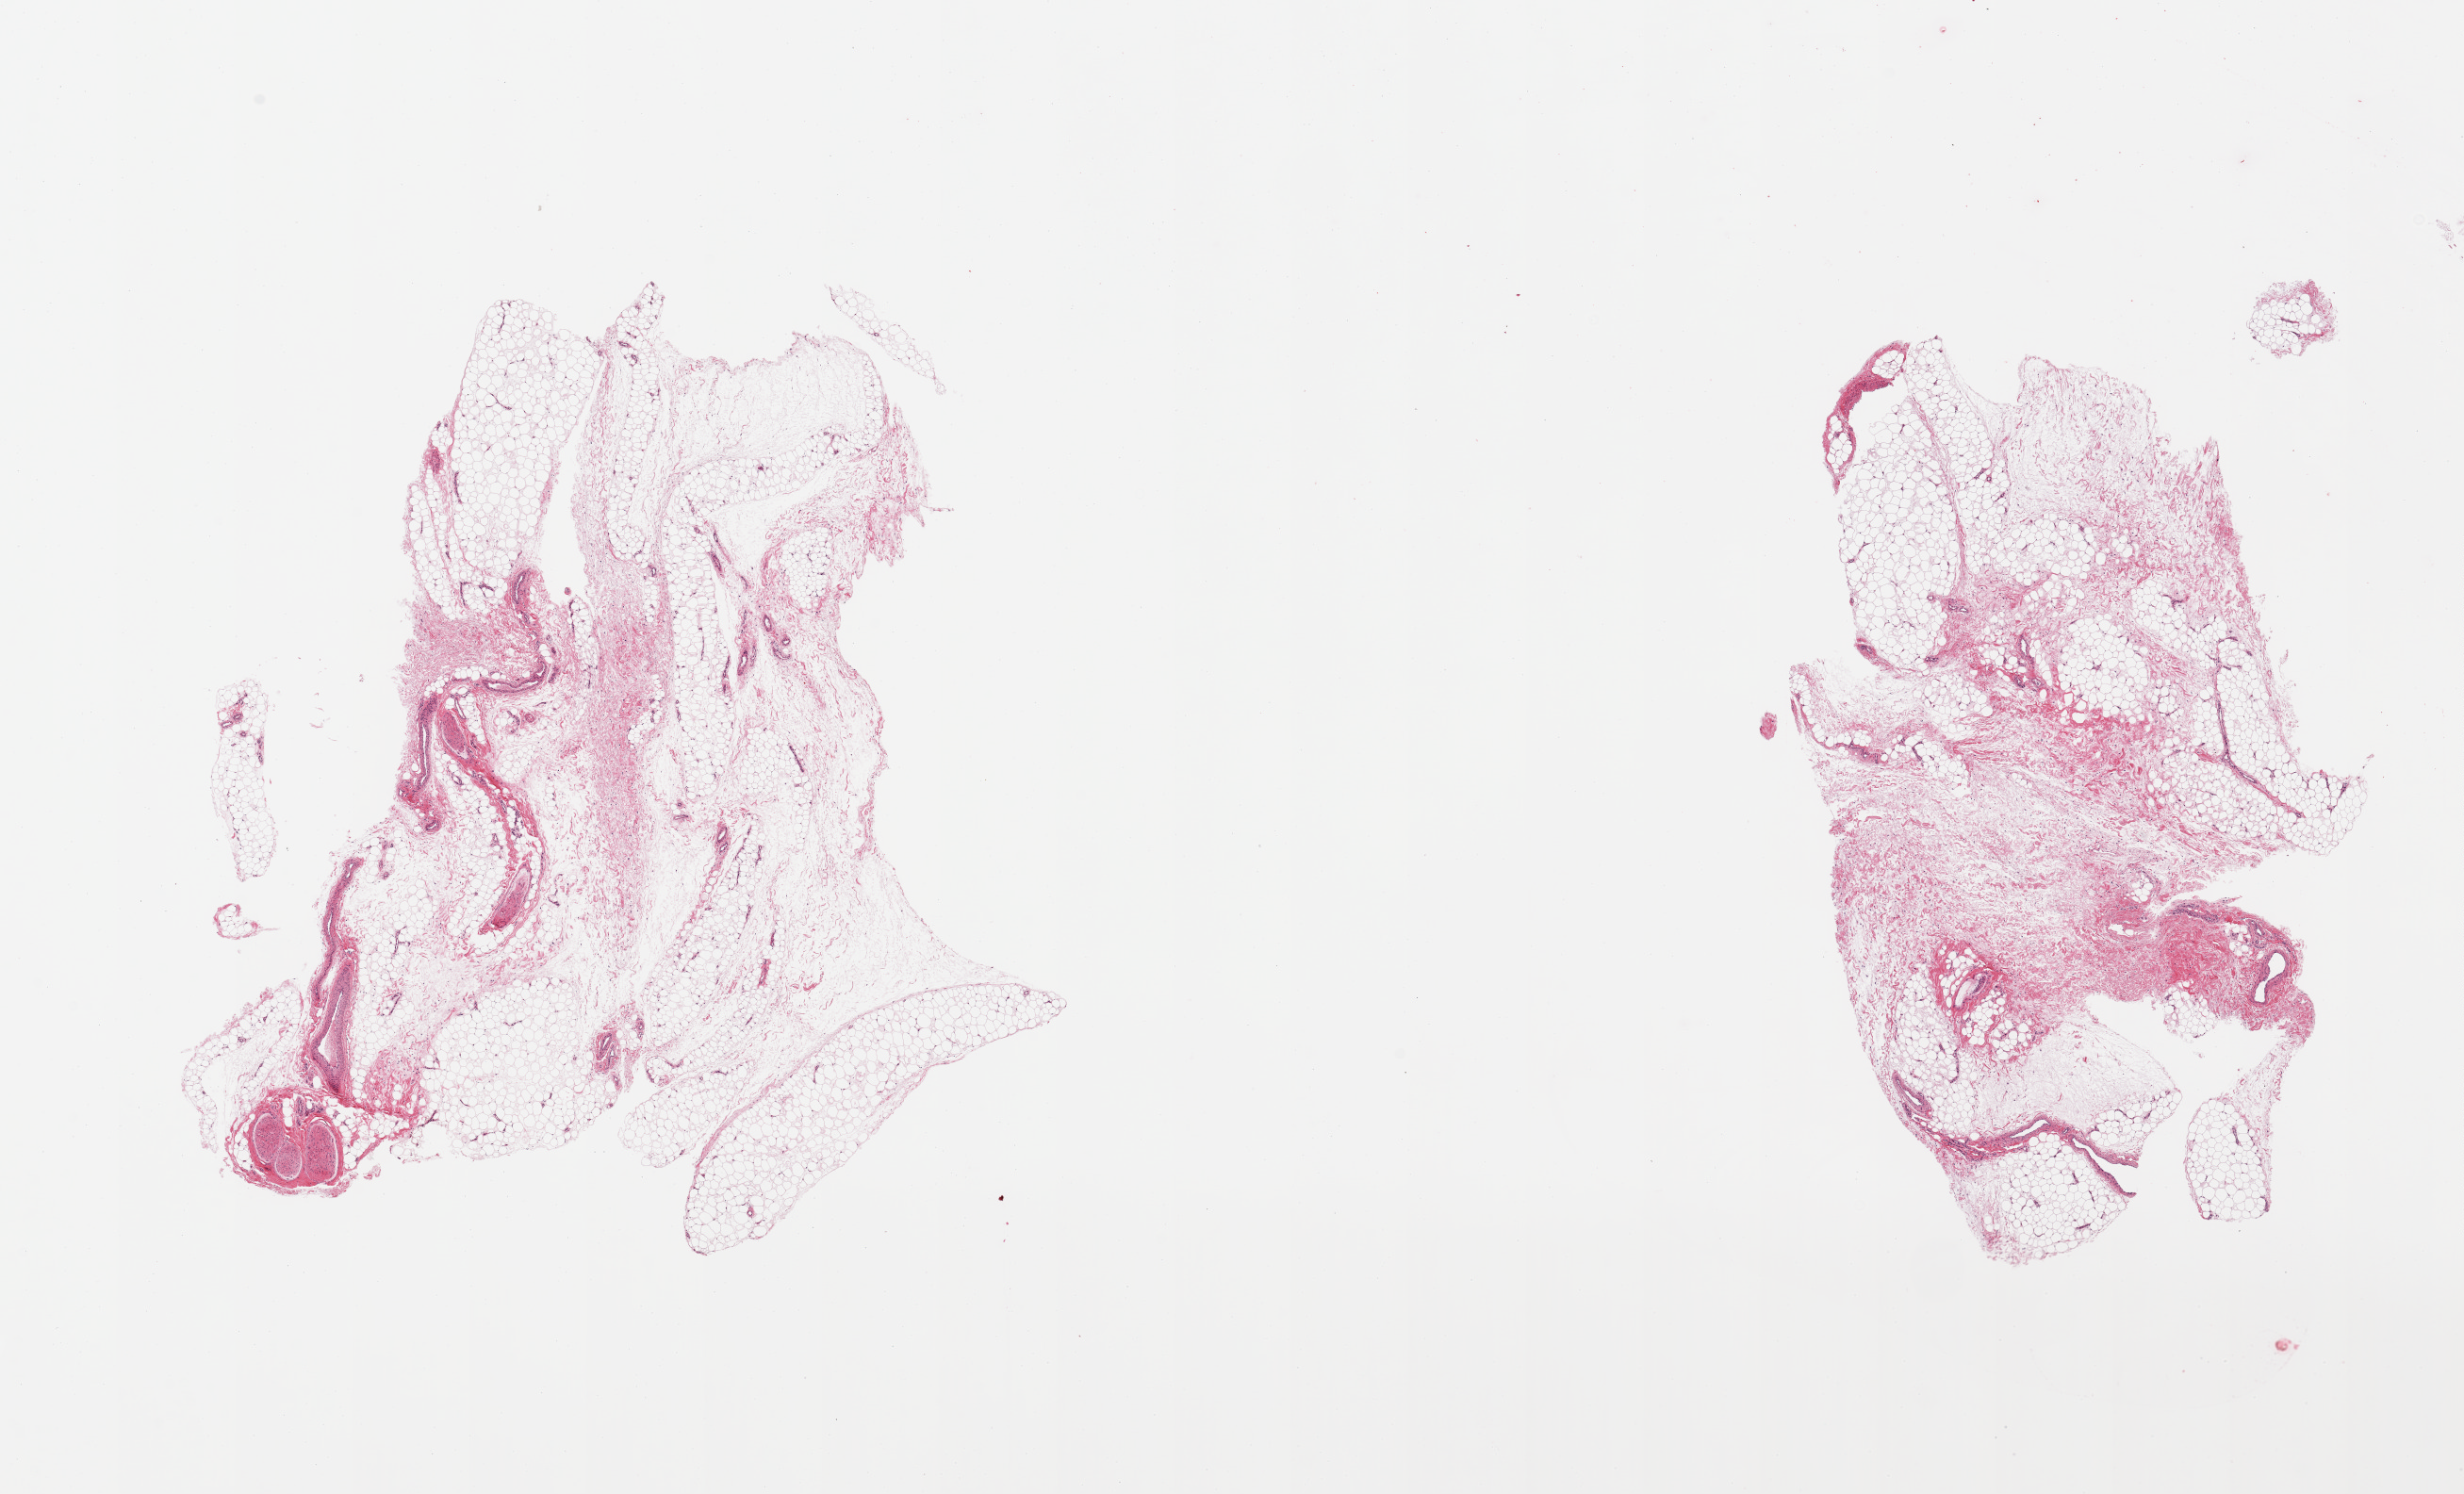
Digitized H&E-stained section, low-resolution overview of the scanned area, about 20.7 x 12.5 mm (slide scanned at 20x); PAXgene-fixed paraffin-embedded (PFPE) section; section of adipose tissue (target tissue); tissue donor sample. Donor: male.
Reviewer comment on this tissue sample: 2 pieces, ~20% vascular, fascia, peripheral nerve elements.